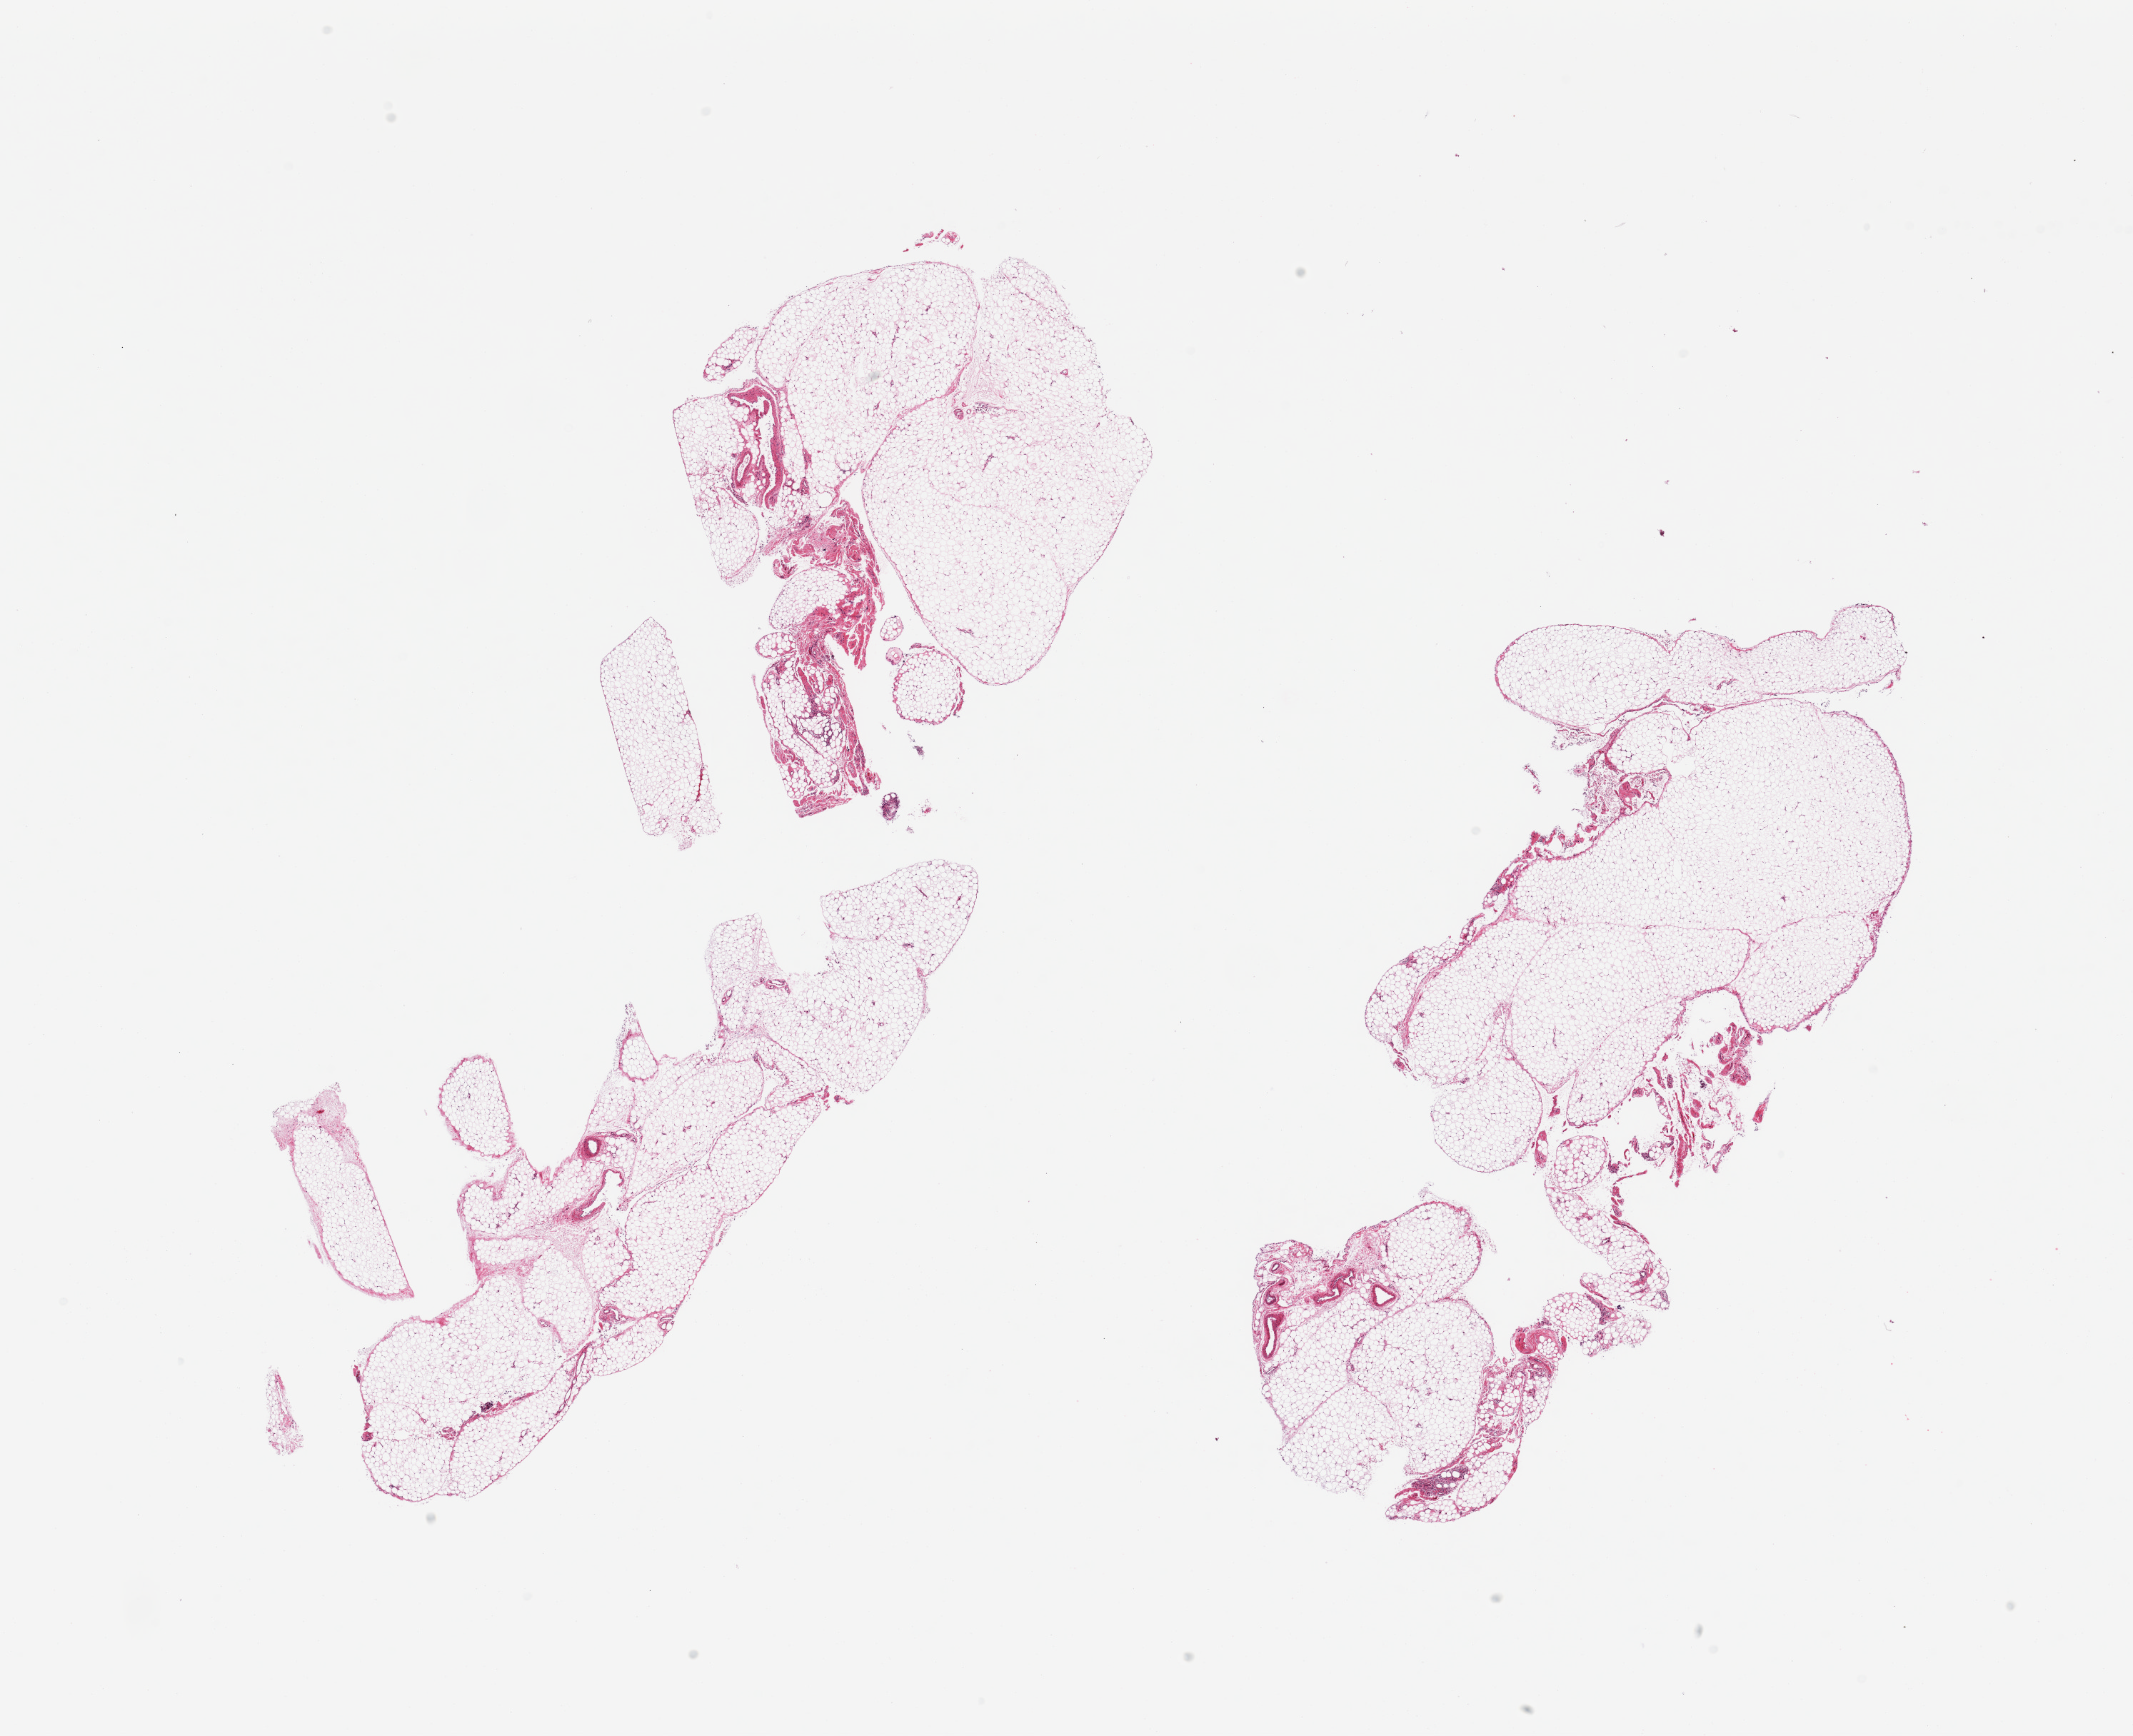
Digitized hematoxylin and eosin (H&E)-stained section — a low-resolution overview of the entire scanned area, about 23.6 x 19.2 mm (acquisition: 20x scan); PAXgene-fixed paraffin-embedded (PFPE) section; target tissue: omentum; tissue donor sample. Female donor.
Pathologist's review note for this sample: 2 pieces, mesothelial hyerplasia/vascular elements 5-10% of tissue.